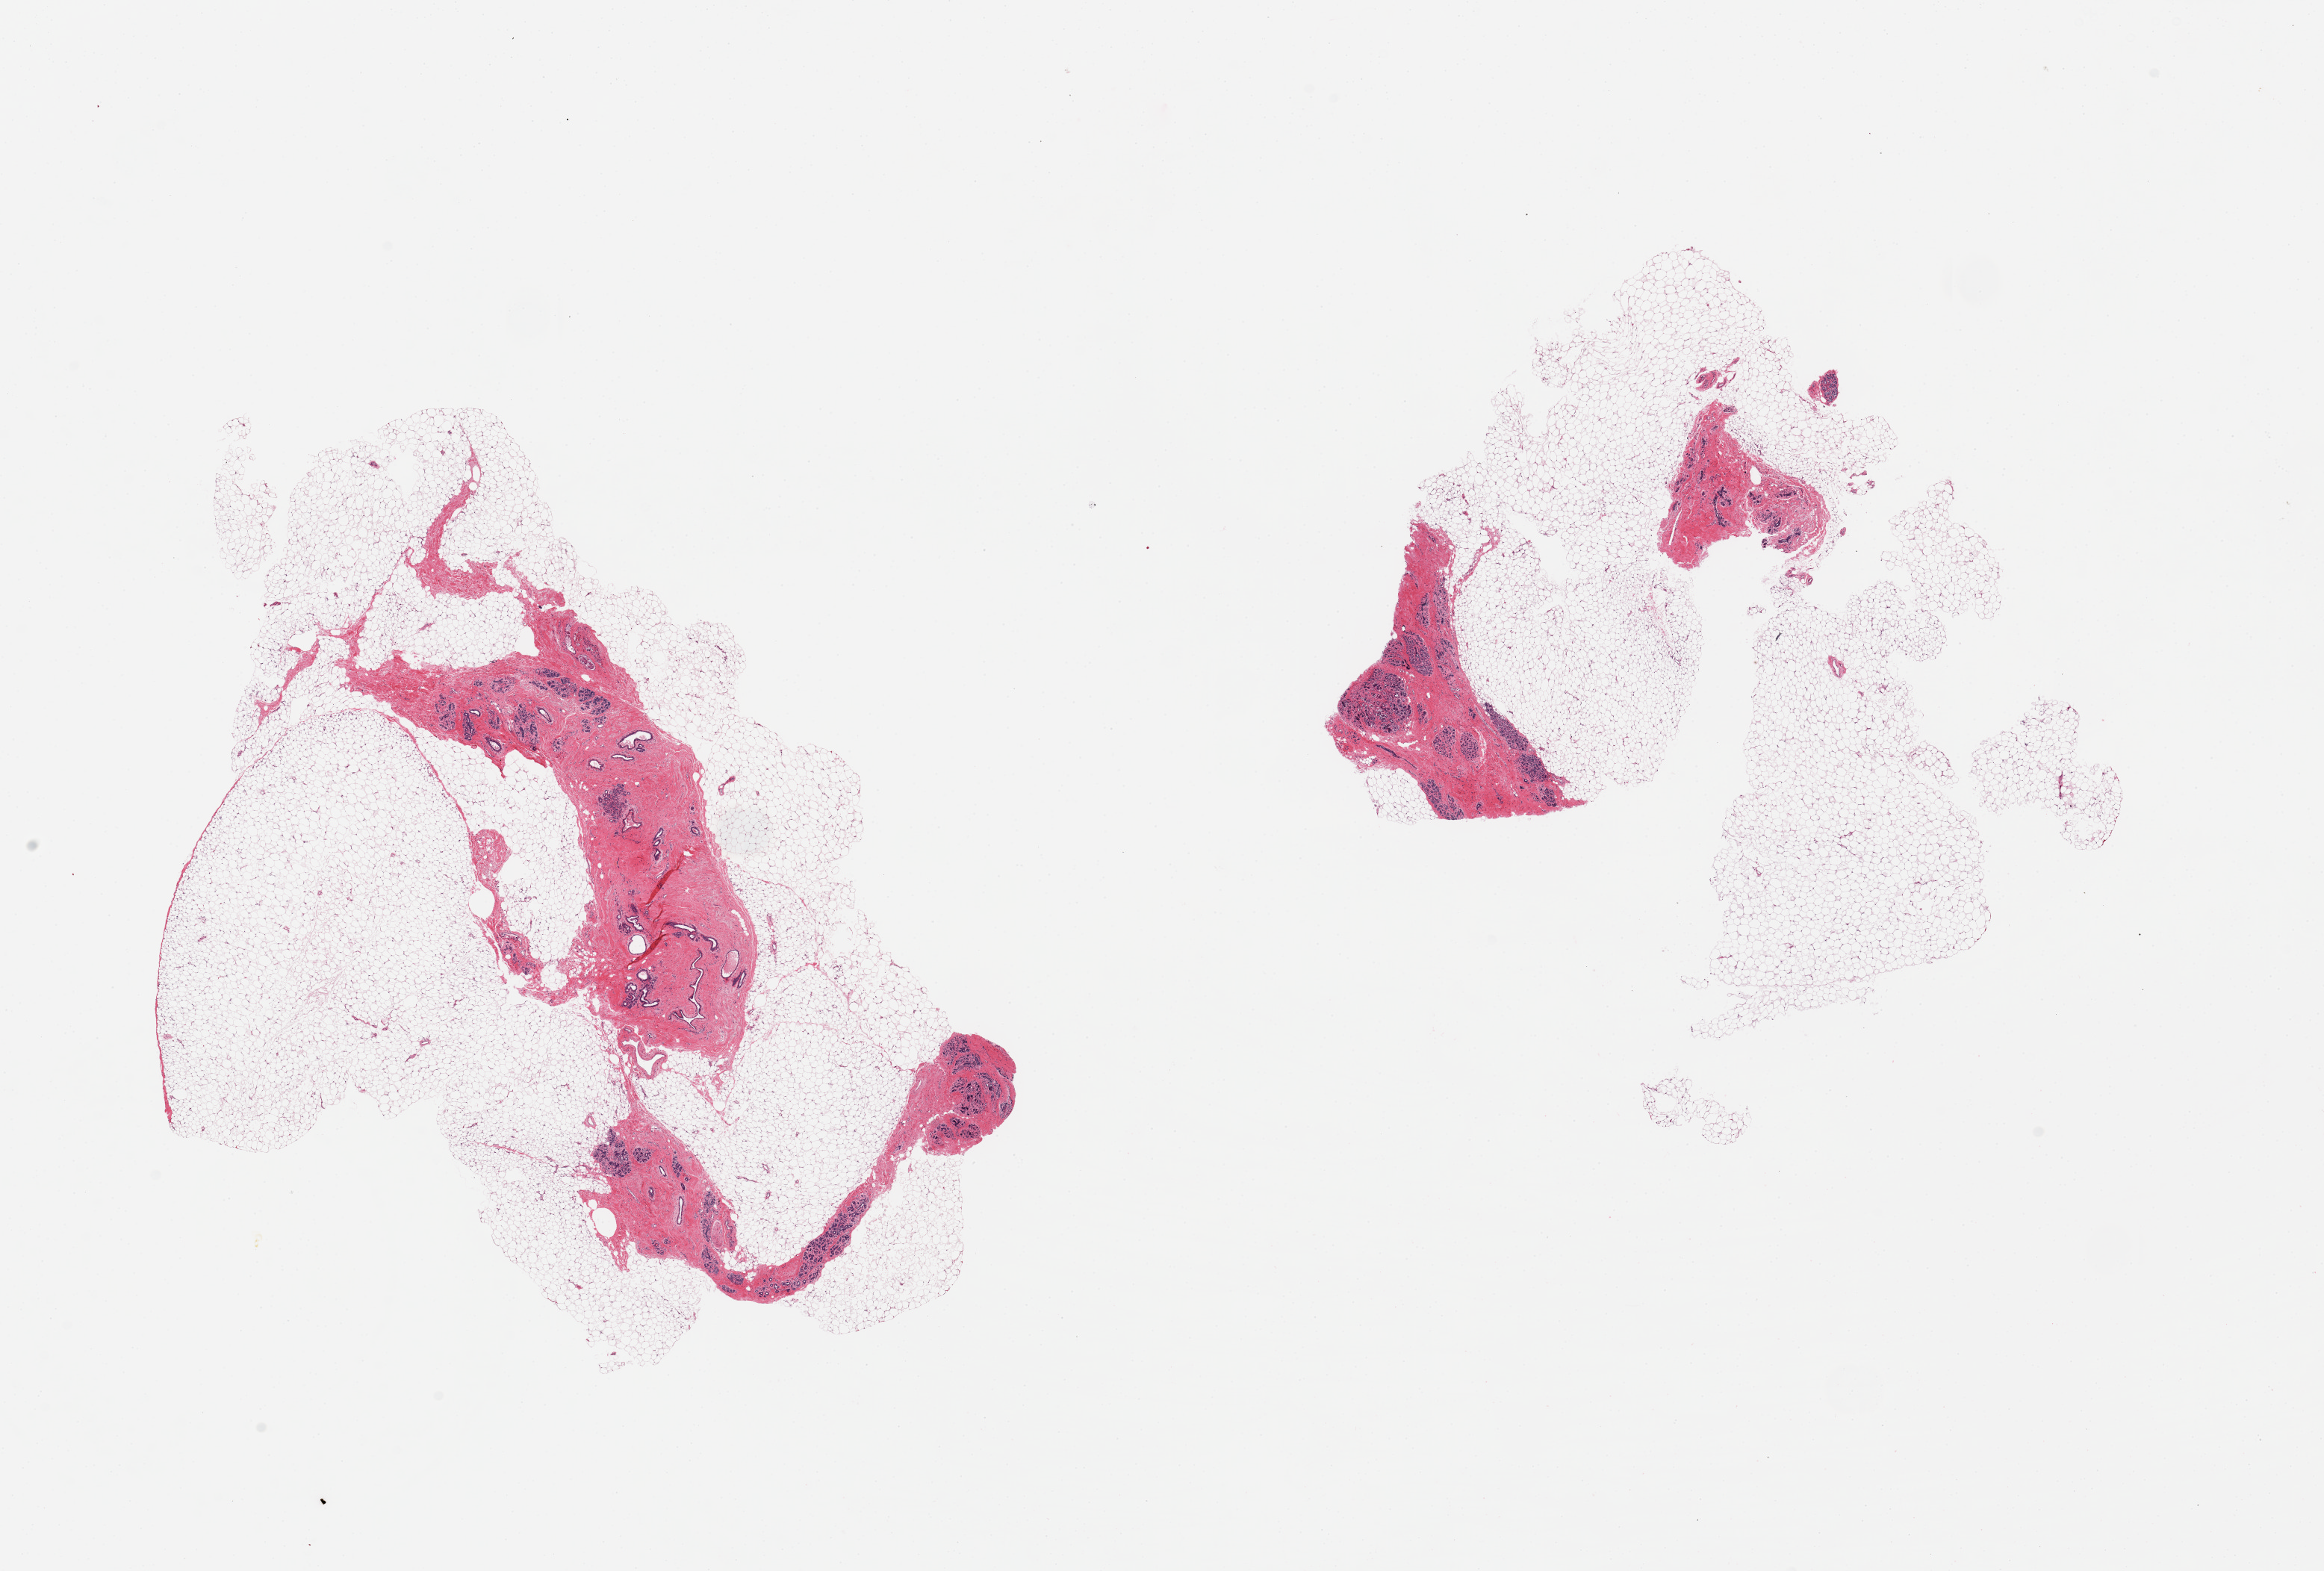
Haematoxylin and eosin whole-slide image, whole scanned area (about 24.6 x 16.6 mm) shown as a low-resolution overview, PAXgene-fixed paraffin-embedded (PFPE) section, section of breast (target tissue), donor tissue sample.
Pathologist's review note for this sample: 2 pieces; ducts and lobules present; 70% adipose content.